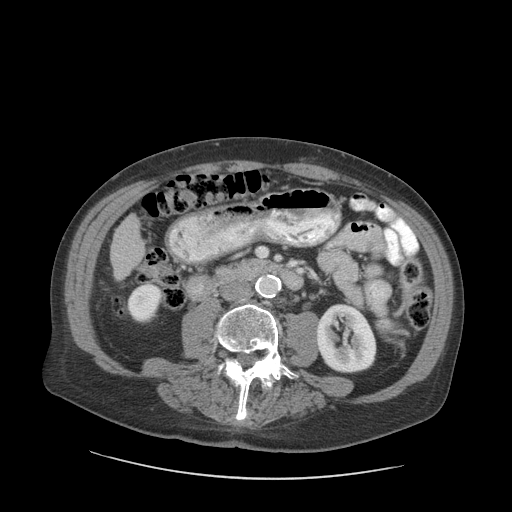
Contrast-enhanced abdominal CT (liver protocol), one axial slice. Reconstruction kernel STANDARD. 140 kVp. Soft-tissue window (W 400 / L 40 HU). 2.5 mm slice thickness. 512 × 512 image matrix. Case-level facts recorded for this patient, not image findings: diagnosis: hepatocellular carcinoma (patient treated with transarterial chemoembolisation; whether this scan precedes or follows treatment is not stated here); TNM stage (as recorded): Stage-I; Child-Pugh class: A; tumour nodularity: uninodular.
Outlined on this slice (semi-automatic segmentation, software-assisted and operator-edited):
- liver parenchyma outside the tumour (the mass and vessels are separate outlines, so this box may not span the whole liver): bounding box (x1, y1, x2, y2) in pixels: (110, 214, 144, 280)